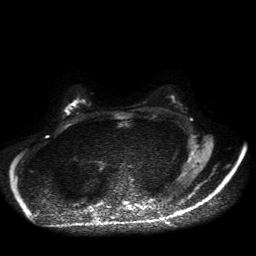
Breast MRI, one axial slice. Slice 27 of 50 in the series (ordered by position). Diffusion-weighted series; image 2 of 4 stored at this slice position (different b-values; order by instance number). 1.5 T. 256 × 256 image matrix, field of view 360 × 360 mm. Female patient.
Annotated regions visible in this slice (manually delineated by an expert):
- tumour on diffusion-weighted imaging: bounding box [x1, y1, x2, y2] px = [65, 107, 72, 112]